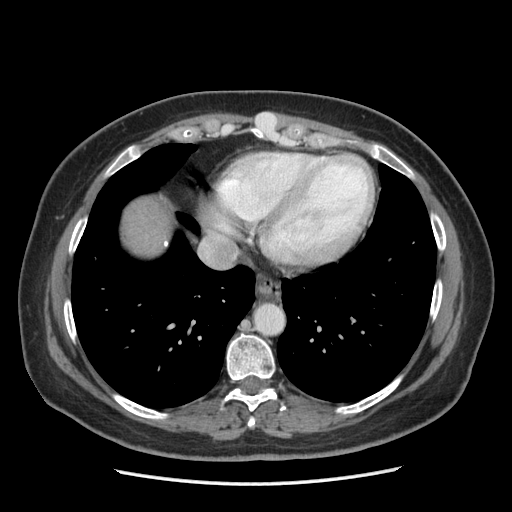
Contrast-enhanced abdominal CT (liver protocol), one axial slice; 140 kVp; soft-tissue window (W 400 / L 40 HU); 2.5 mm slice thickness; 512 × 512 image matrix. Case-level facts recorded for this patient, not image findings: diagnosis: hepatocellular carcinoma (patient treated with transarterial chemoembolisation; whether this scan precedes or follows treatment is not stated here); TNM stage (as recorded): Stage-I; Child-Pugh class: A; tumour differentiation: poorly differentiated; tumour nodularity: uninodular.
Structures marked on this image (semi-automatically segmented with operator editing):
- liver parenchyma outside the tumour (the mass and vessels are separate outlines, so this box may not span the whole liver): bounding box (x1, y1, x2, y2) in pixels: (124, 198, 170, 254)
- liver vessels: (164, 242, 167, 245)